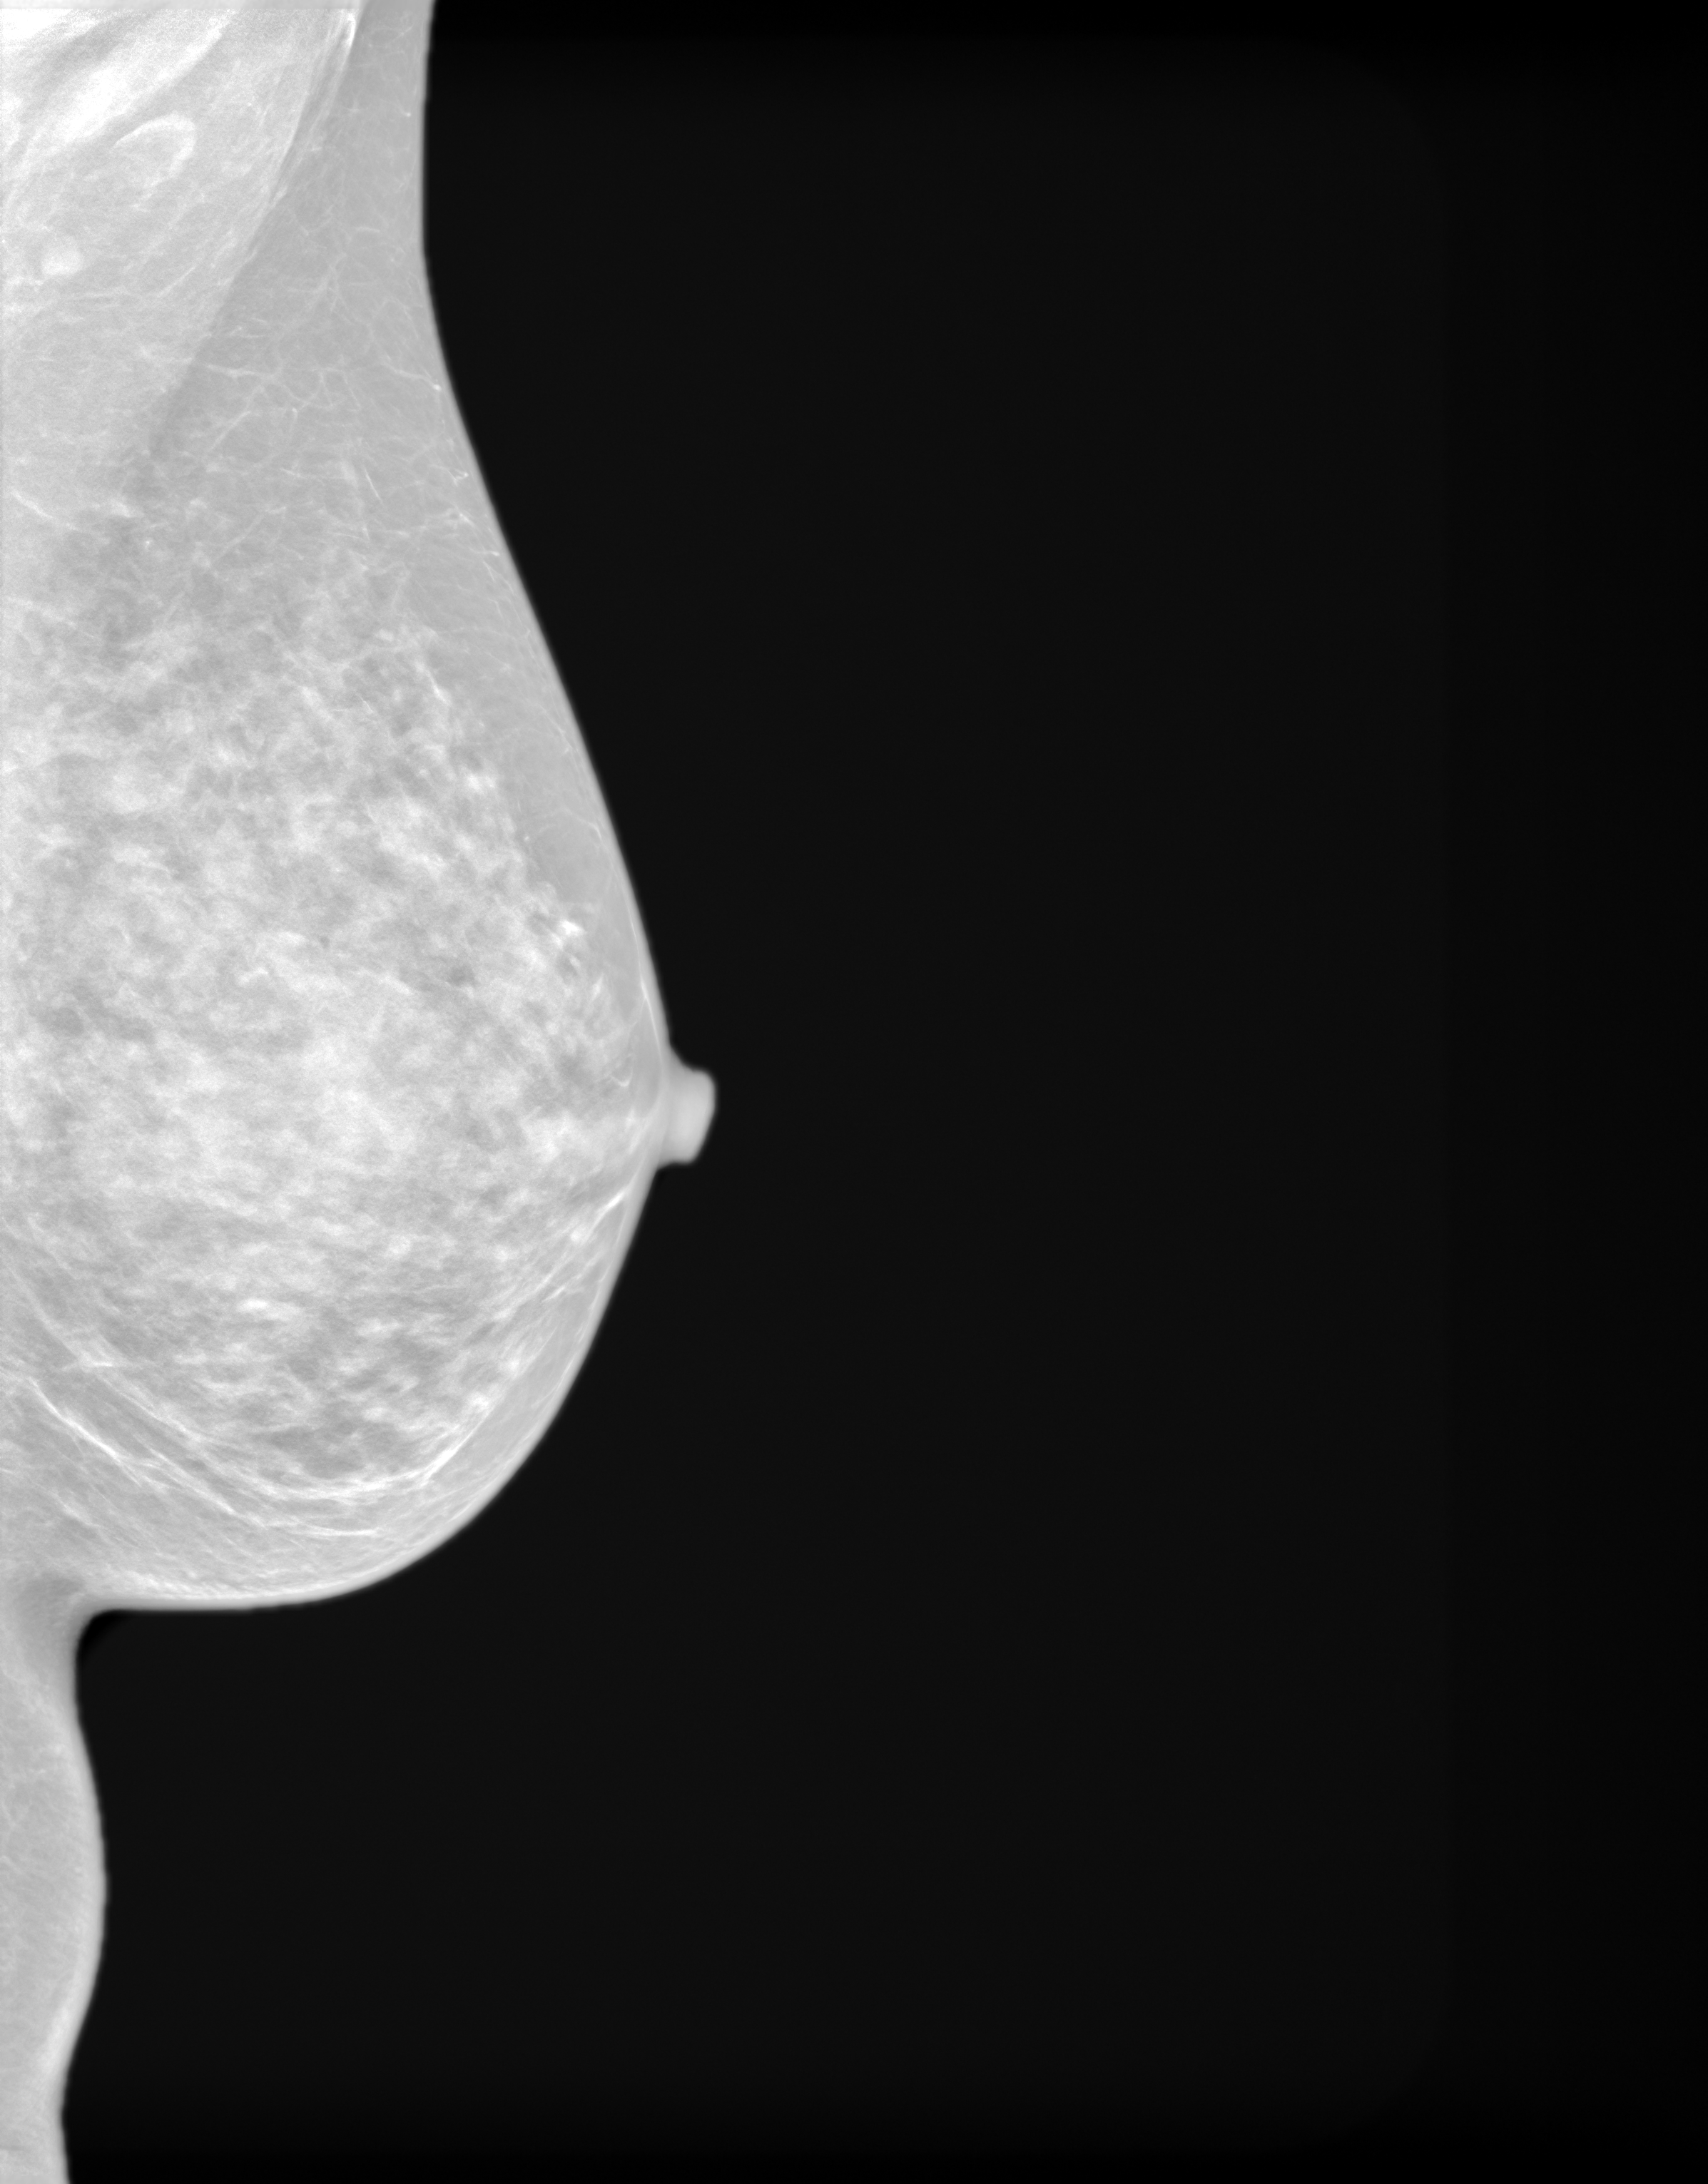
Annual screening mammography examination, system: SenoIris_1SP2(440). Female patient, age 61 years.
Image type: synthesized 2-D view from tomosynthesis. Breast: left. Projection: medio-lateral oblique projection.